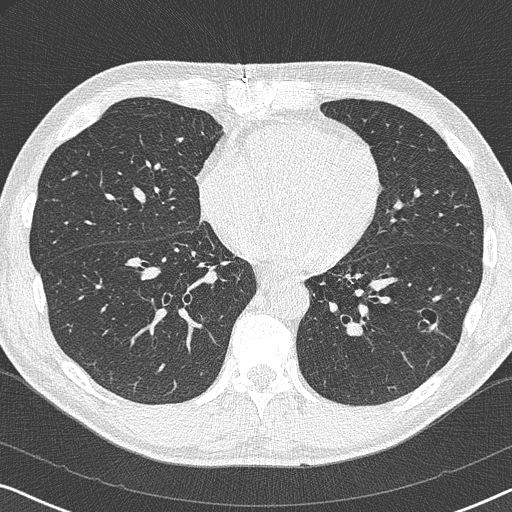
Low-dose screening chest CT, axial slice, baseline screening round, lung window (W 1500 / L -600 HU), 1 mm slice thickness, lung (sharp) reconstruction kernel (B50f). Male participant, aged 59 years at enrolment. Current smoker at enrolment.
- Lesion marked by an expert reader, bounding box [x1, y1, x2, y2] px = [410, 303, 450, 337].
- The screening reader recorded 2 non-calcified nodules or masses ≥4 mm on this exam (left lower lobe, right middle lobe); which of them this box marks is not recorded.